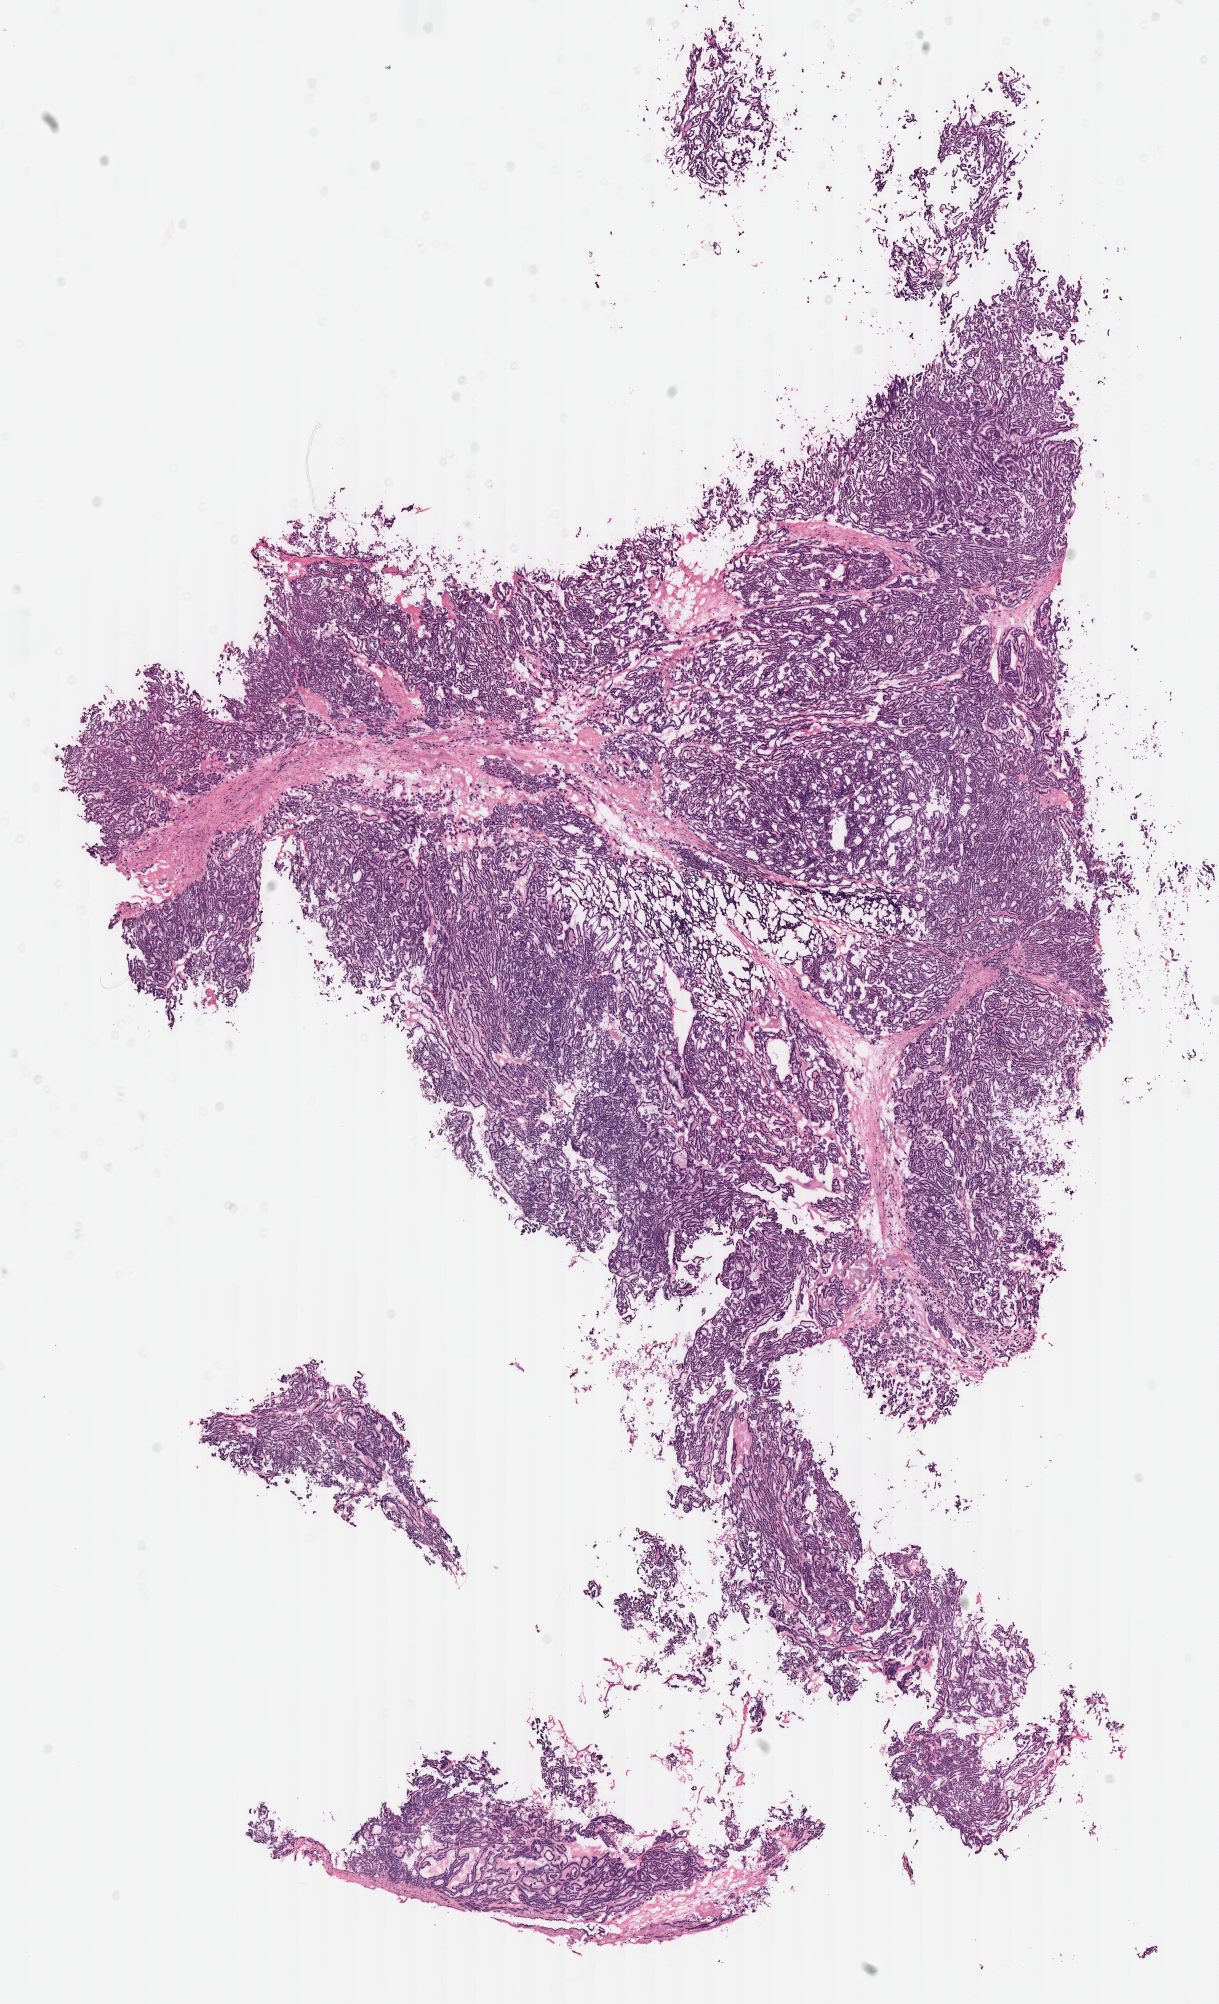
H&E-stained whole-slide image — shown as a low-resolution overview of the whole scanned area (about 9.6 x 15.8 mm, from a 40x scan), frozen section, primary tumour sample from the kidney. Patient: female, age at initial diagnosis 58 years. Pathologist review of this section (percent, as recorded): tumour cells 95%, tumour nuclei 95%, normal cells 0%, stromal cells 5%, necrosis 0%.
AJCC pathologic stage: I (7th edition). Histologic diagnosis: Papillary adenocarcinoma, NOS.